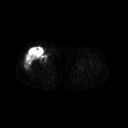
FDG PET of an extremity soft-tissue mass (from a PET/CT study), one axial slice. Slice 235 of 311 in the series (ordered by position). 3.27 mm slice thickness. 128 × 128 image matrix. Female patient, age 57 years. From the clinical record (not read from this slice): histological type: pleiomorphic undifferentiated sarcoma; grade: high; site of the primary tumour: right quadricep.
Structures marked on this image (expert contour drawn on MRI and transferred to this co-registered scan by the dataset authors):
- tumour plus oedema (research contour): box from (x=25, y=49) to (x=46, y=71) px
- tumour (research contour): (x=25, y=49)–(x=46, y=71)